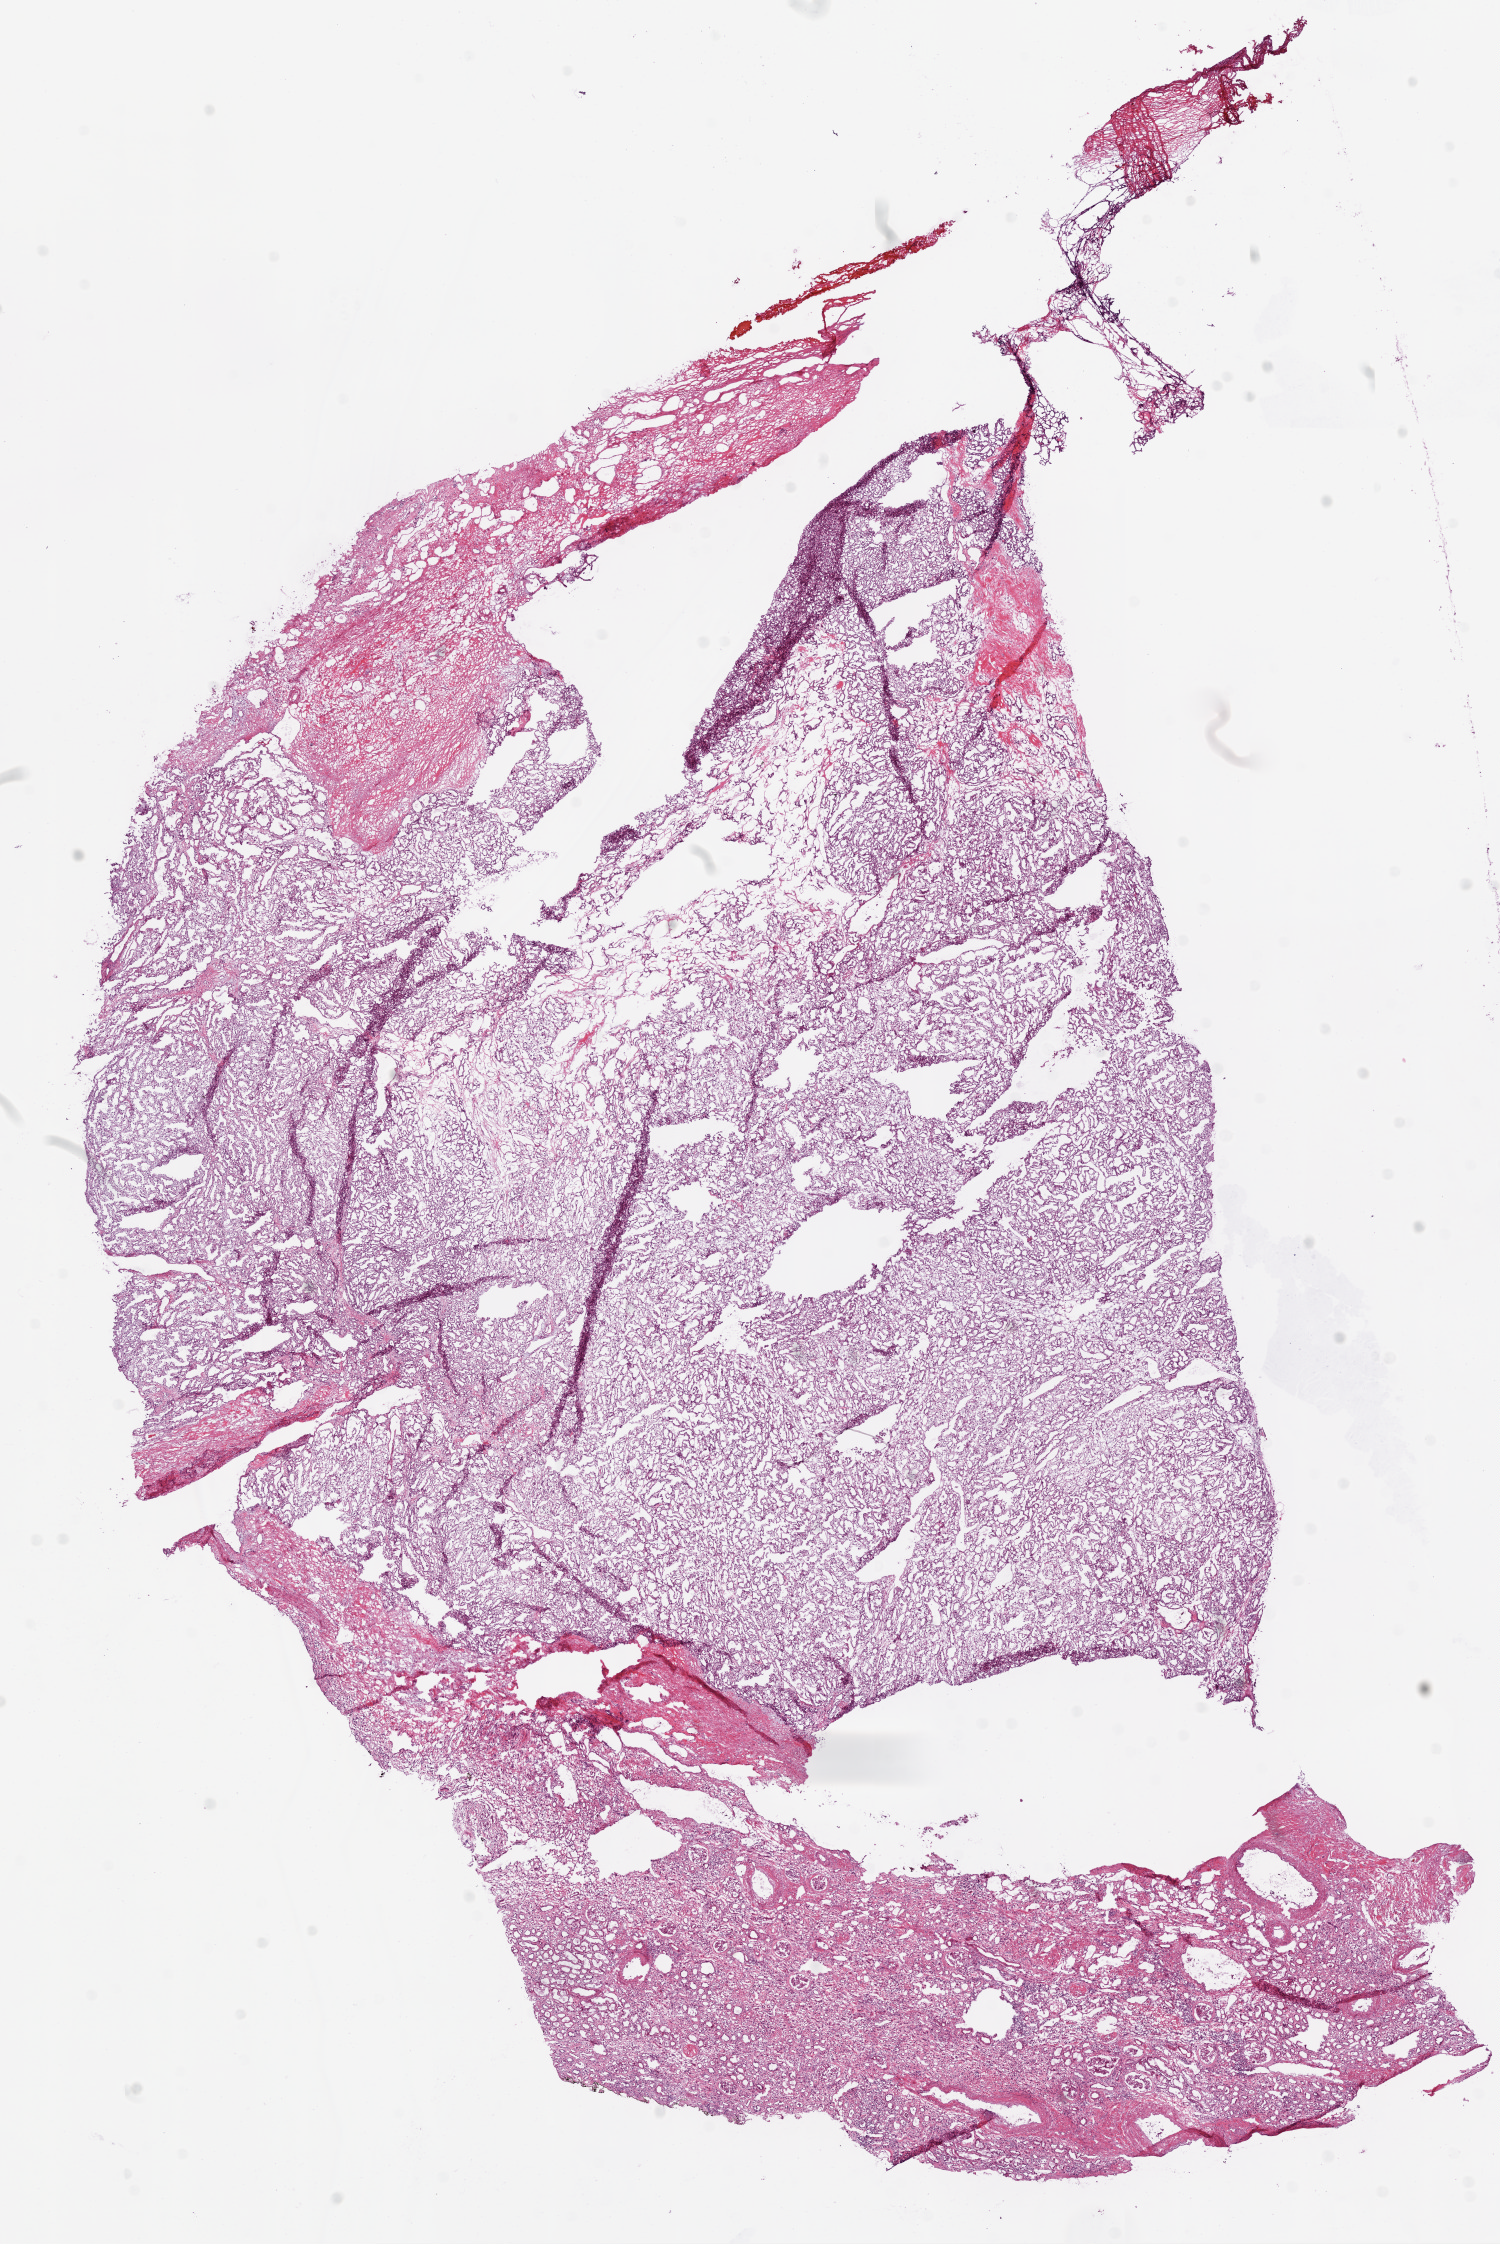
H&E whole-slide image, whole scanned area (about 12.0 x 18.0 mm) shown as a low-resolution overview. Frozen section. Primary tumour sample from the kidney. Patient: male, age at initial diagnosis 65 years. Histologic grade: G2 (moderately differentiated). Slide review estimates, as recorded: tumour cells 65%, tumour nuclei 70%, normal cells 25%, stromal cells 20%, necrosis 0%.
AJCC pathologic stage: I. Pathologic diagnosis: Clear cell adenocarcinoma, NOS.